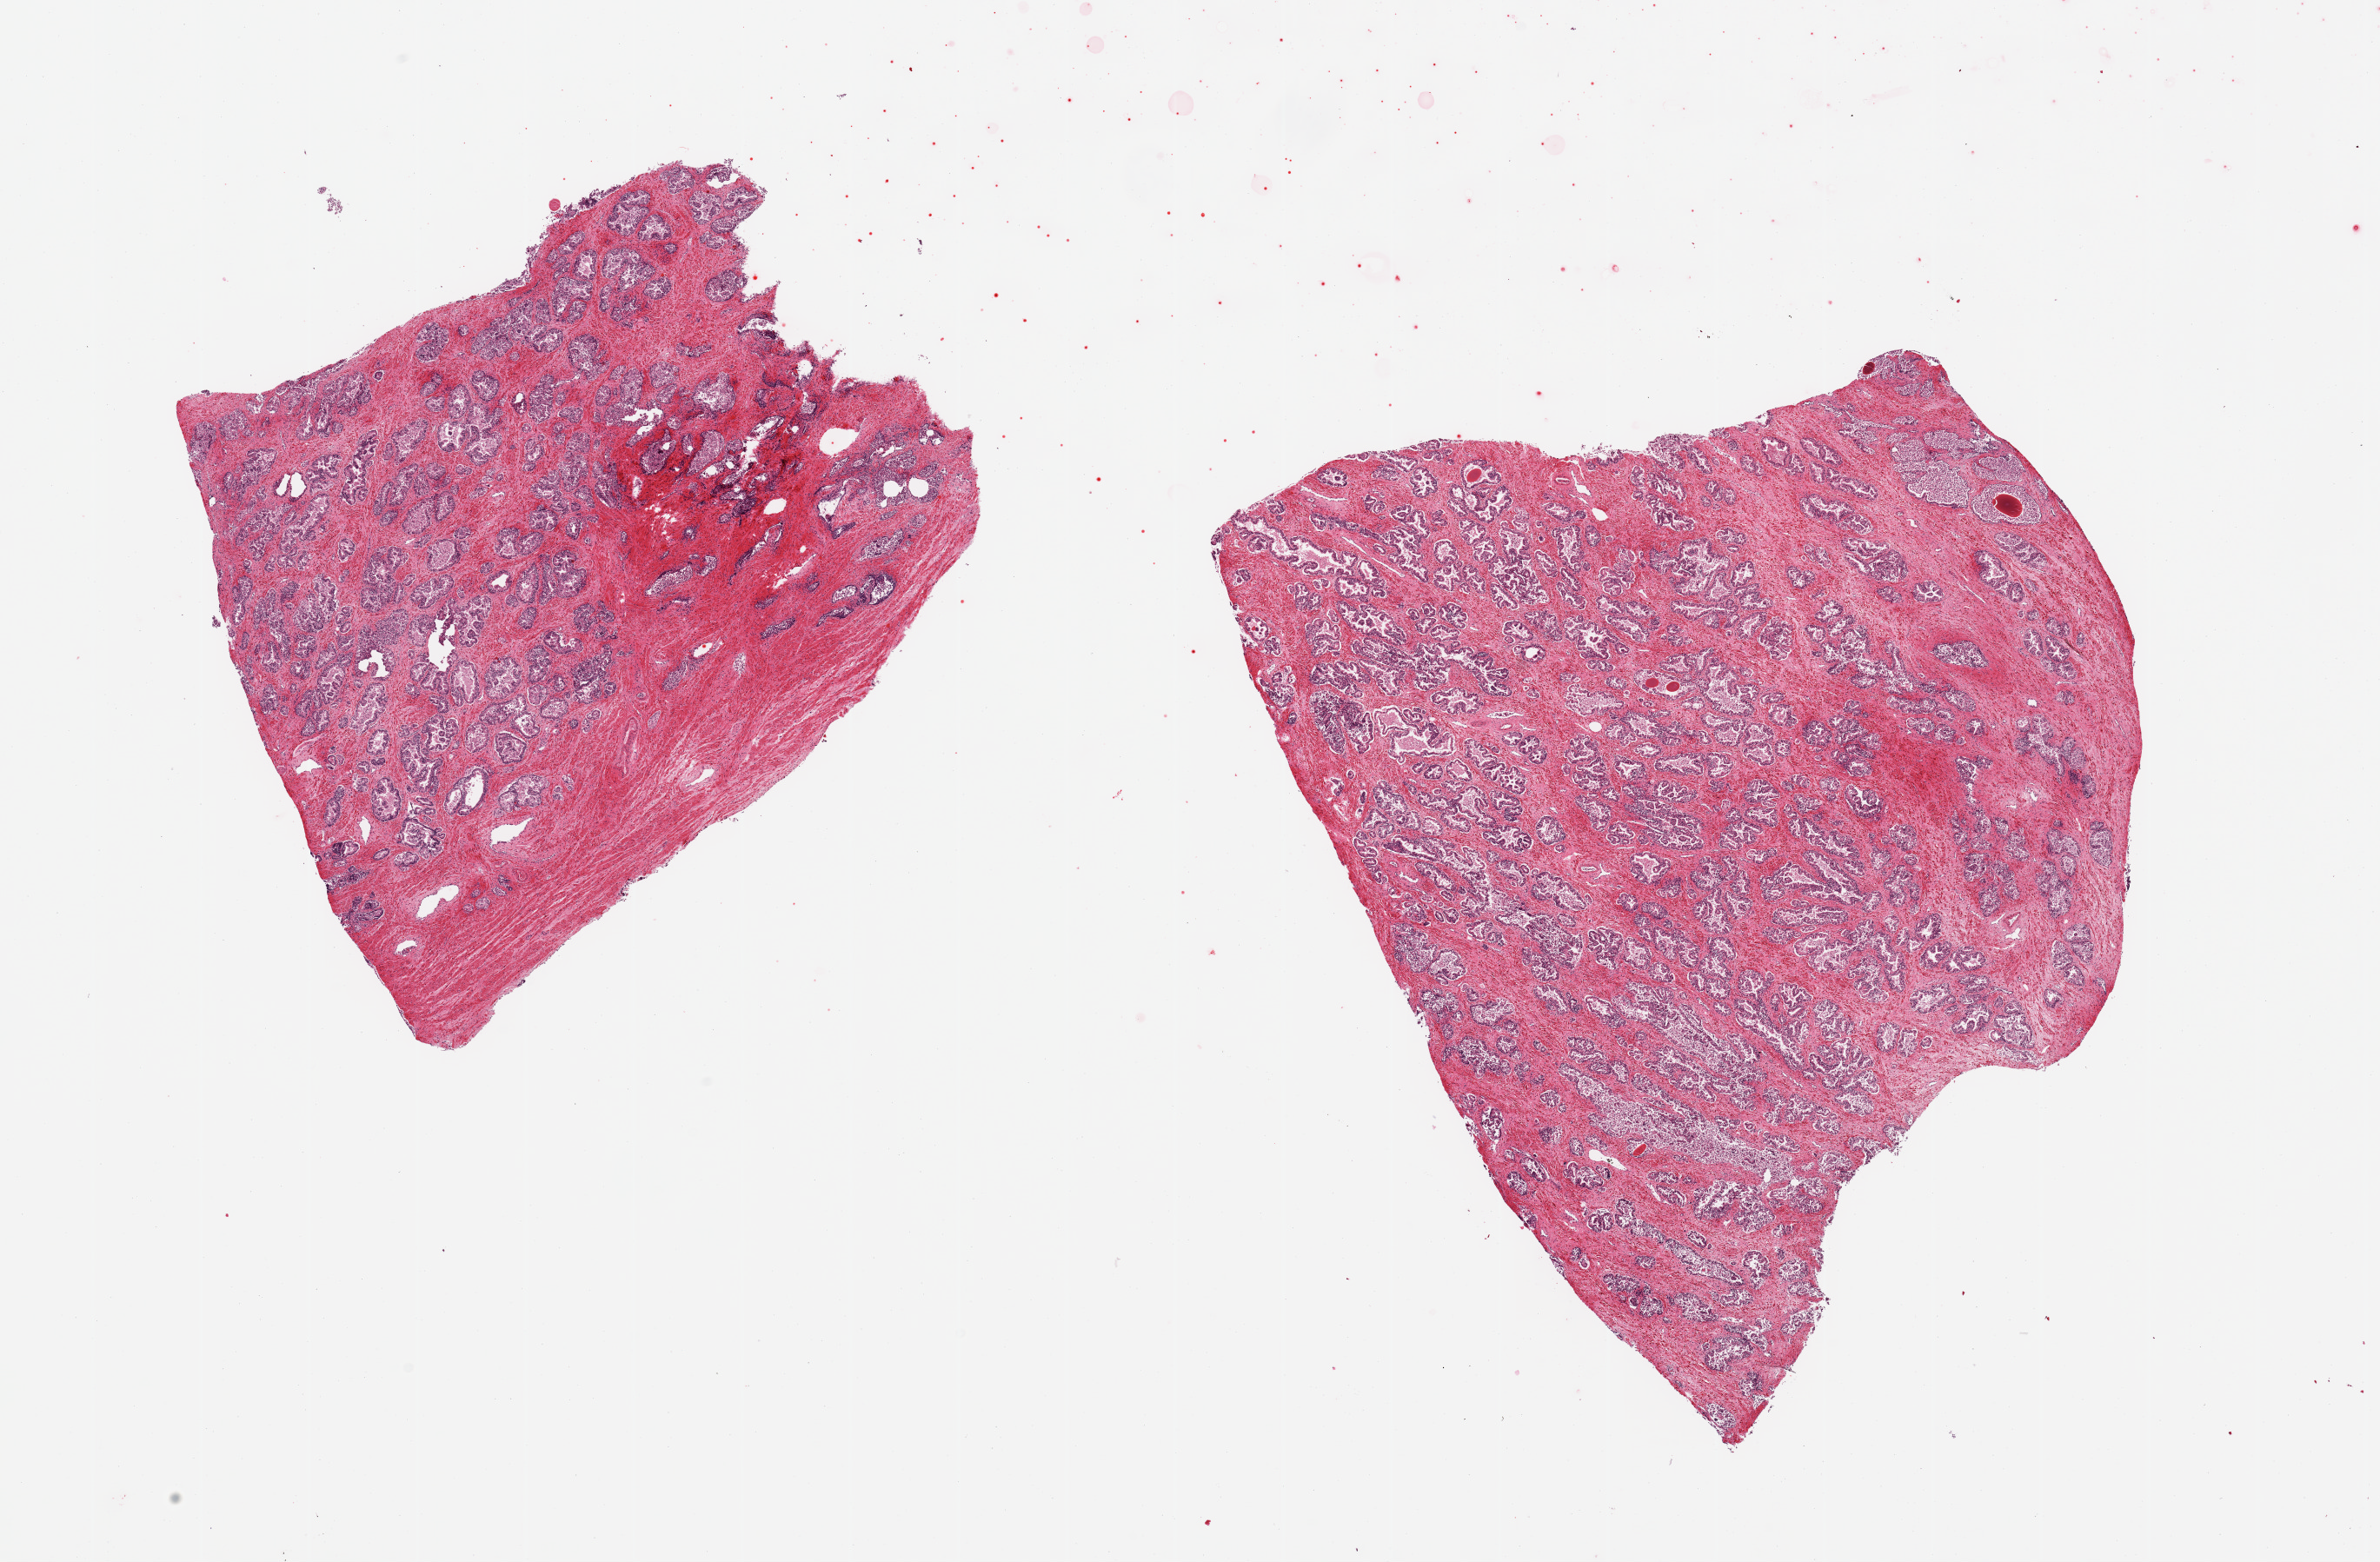
H&E whole-slide image, brightfield, shown as a low-resolution overview of the whole scanned area (about 21.7 x 14.2 mm, from a 20x scan); PAXgene-fixed, paraffin-embedded tissue; target tissue: prostate; tissue donor sample.
Pathologist's review note for this sample: 2 pieces, glandular elements approaching score '2' in some foci but resaonably well preserved.